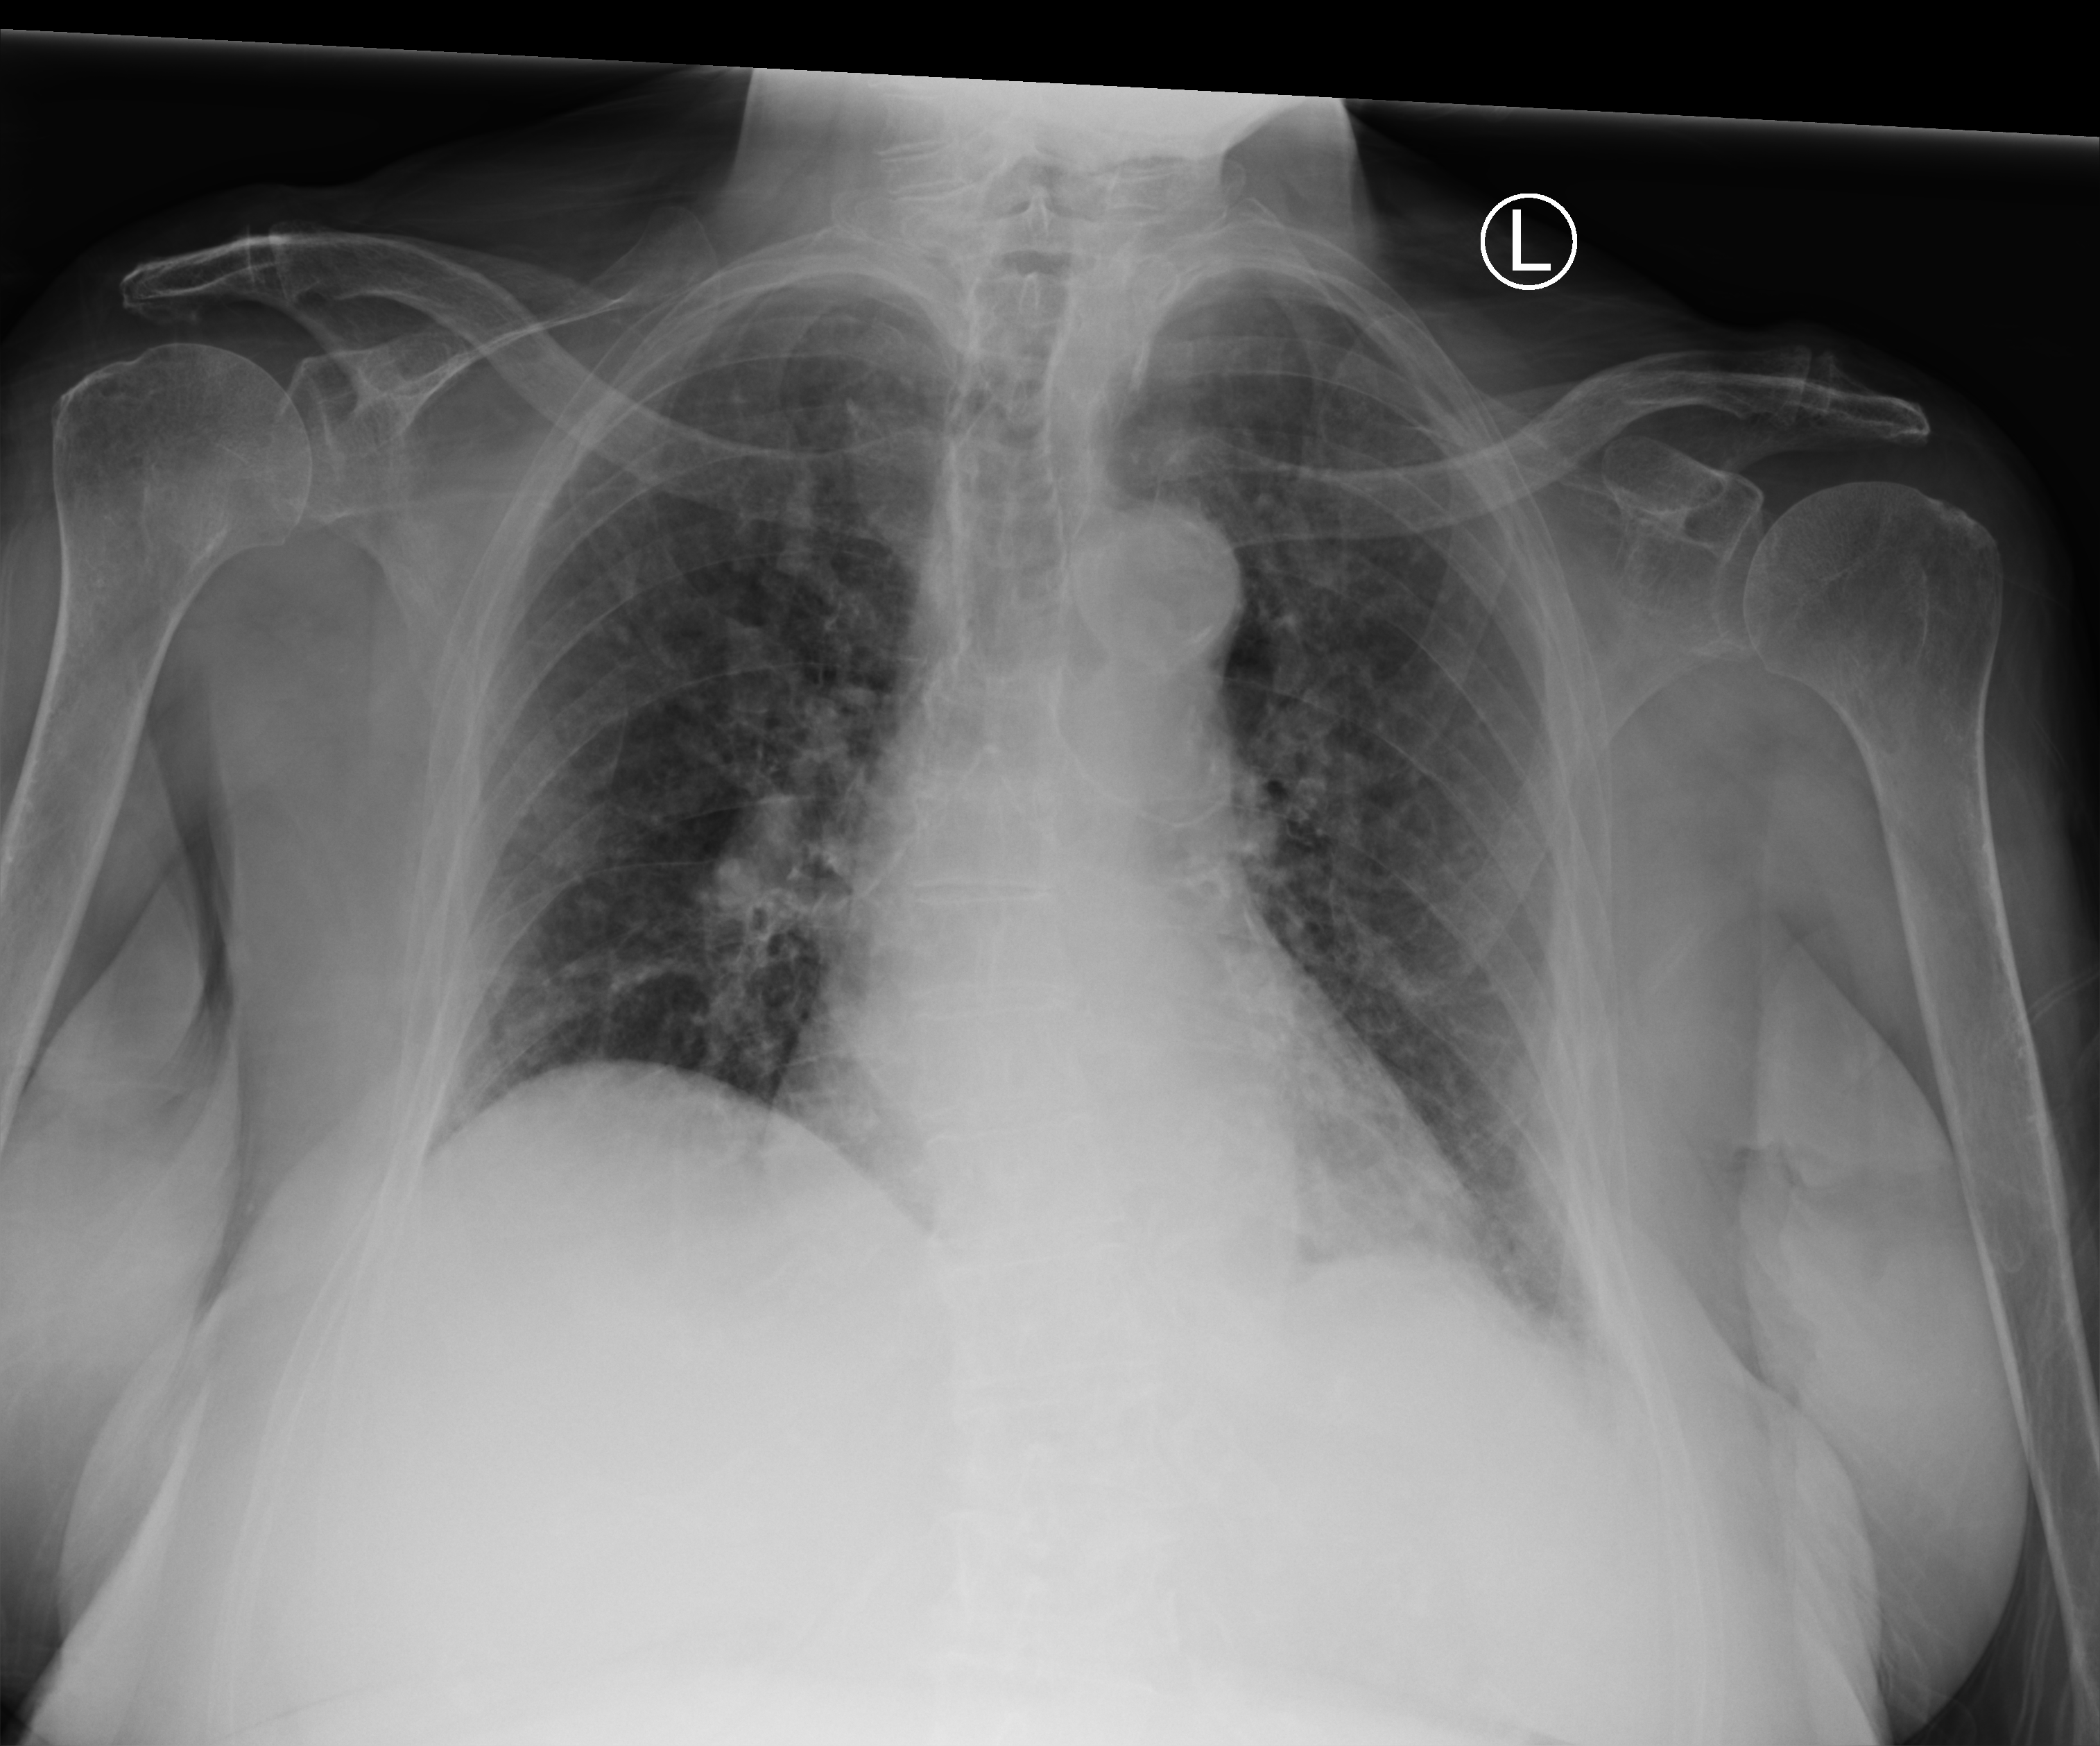
Portable chest radiograph, anteroposterior (AP) projection. Female patient hospitalised with COVID-19, age 75–90 years.
Admission-level facts for this patient (not findings on this image; timing relative to this image not recorded):
- mechanically ventilated during this hospital stay: no
- smoking status (admission record): never
- admitted to intensive care during this hospital stay: no